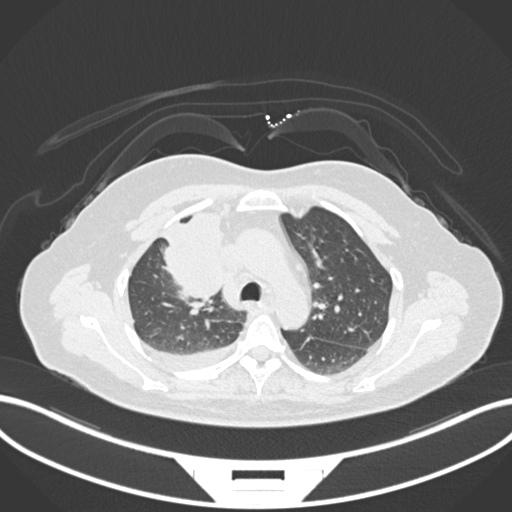
Chest CT, one axial slice. Position 110 of 172 along the scan axis. 120 kVp. Lung window (W 1500 / L -600 HU). 512 × 512 image matrix. Patient: female, 52 years. From the clinical record (not read from this slice): clinical TNM (as recorded): T3 N1 M1.
Annotated regions visible in this slice (bounding box drawn by a radiologist):
- lung tumour (recorded histology: adenocarcinoma): box from (x=155, y=207) to (x=227, y=306) px